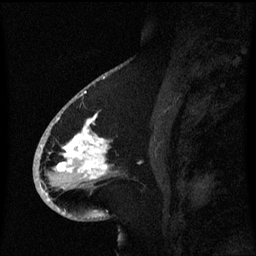
Breast MRI (dynamic contrast-enhanced), one sagittal slice; slice 32 of 60 in the series (ordered by position); dynamic contrast-enhanced series, image 2 of 3 at this slice position (ordered by acquisition); 1.5 T; TE 4.2 ms, TR 8.4 ms; 2.1 mm slice thickness; 256 × 256 image matrix. Female patient, age 53 years. From the clinical record (not read from this slice): setting: breast cancer imaged before/during neoadjuvant chemotherapy; receptor status: HR-positive, HER2-negative.
Outlined on this slice (semi-automatic segmentation, software-assisted and operator-edited):
- analysis volume of interest (the breast-tissue region the enhancement analysis was run in; not a lesion): bounding box <49,108,120,201> (left, top, right, bottom; pixels)
- tumour enhancement mask (voxels above the 70 % enhancement threshold inside the analysis volume of interest): <57,116,110,179>